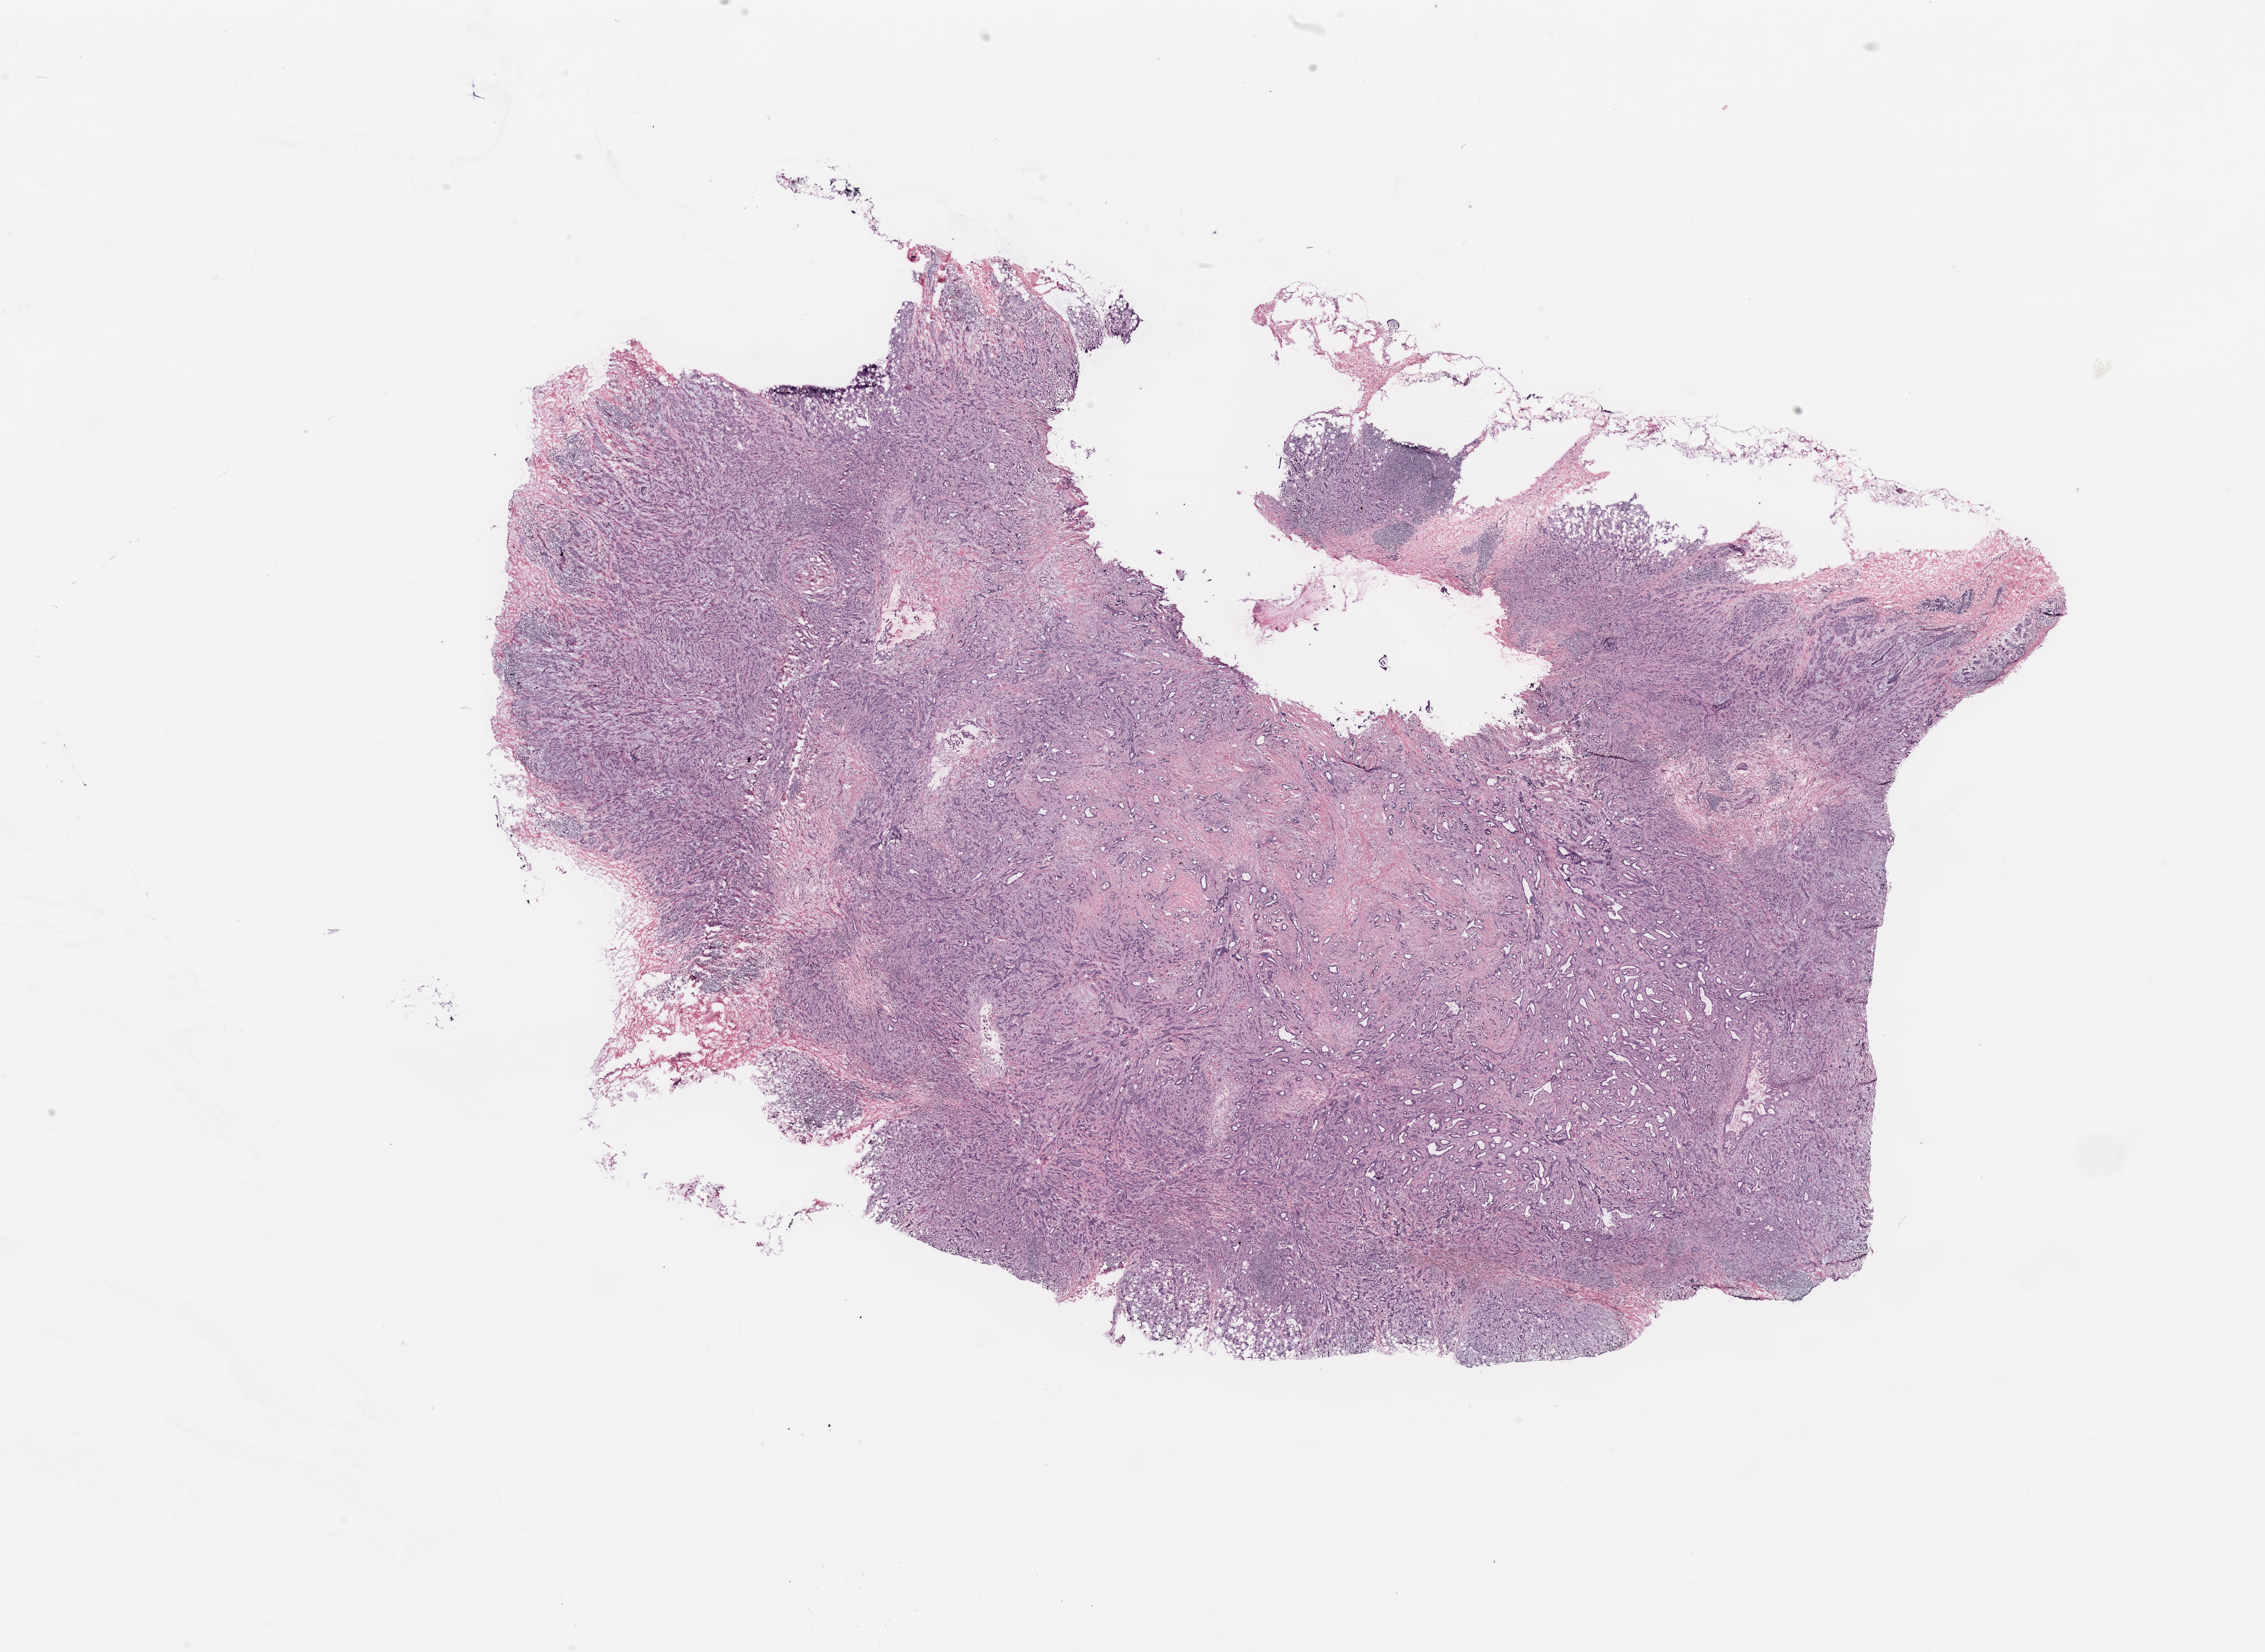
Whole-slide histology image, H&E — a low-resolution overview of the entire scanned area, about 27.6 x 20.1 mm (slide scanned at 20x), breast, tissue type not recorded.
Patient diagnosis (cohort enrolment): breast cancer (breast).